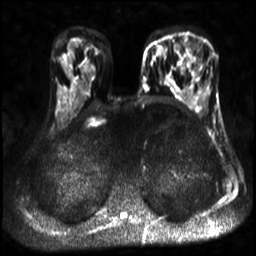
Breast MRI, one axial slice; position 16 of 30 along the scan axis; diffusion-weighted series; image 2 of 4 stored at this slice position (different b-values; order by instance number); 3 T; 256 × 256 image matrix. Female patient.
Annotated regions visible in this slice (outlined manually by an expert reader):
- tumour on diffusion-weighted imaging: box from (x=180, y=36) to (x=198, y=66) px